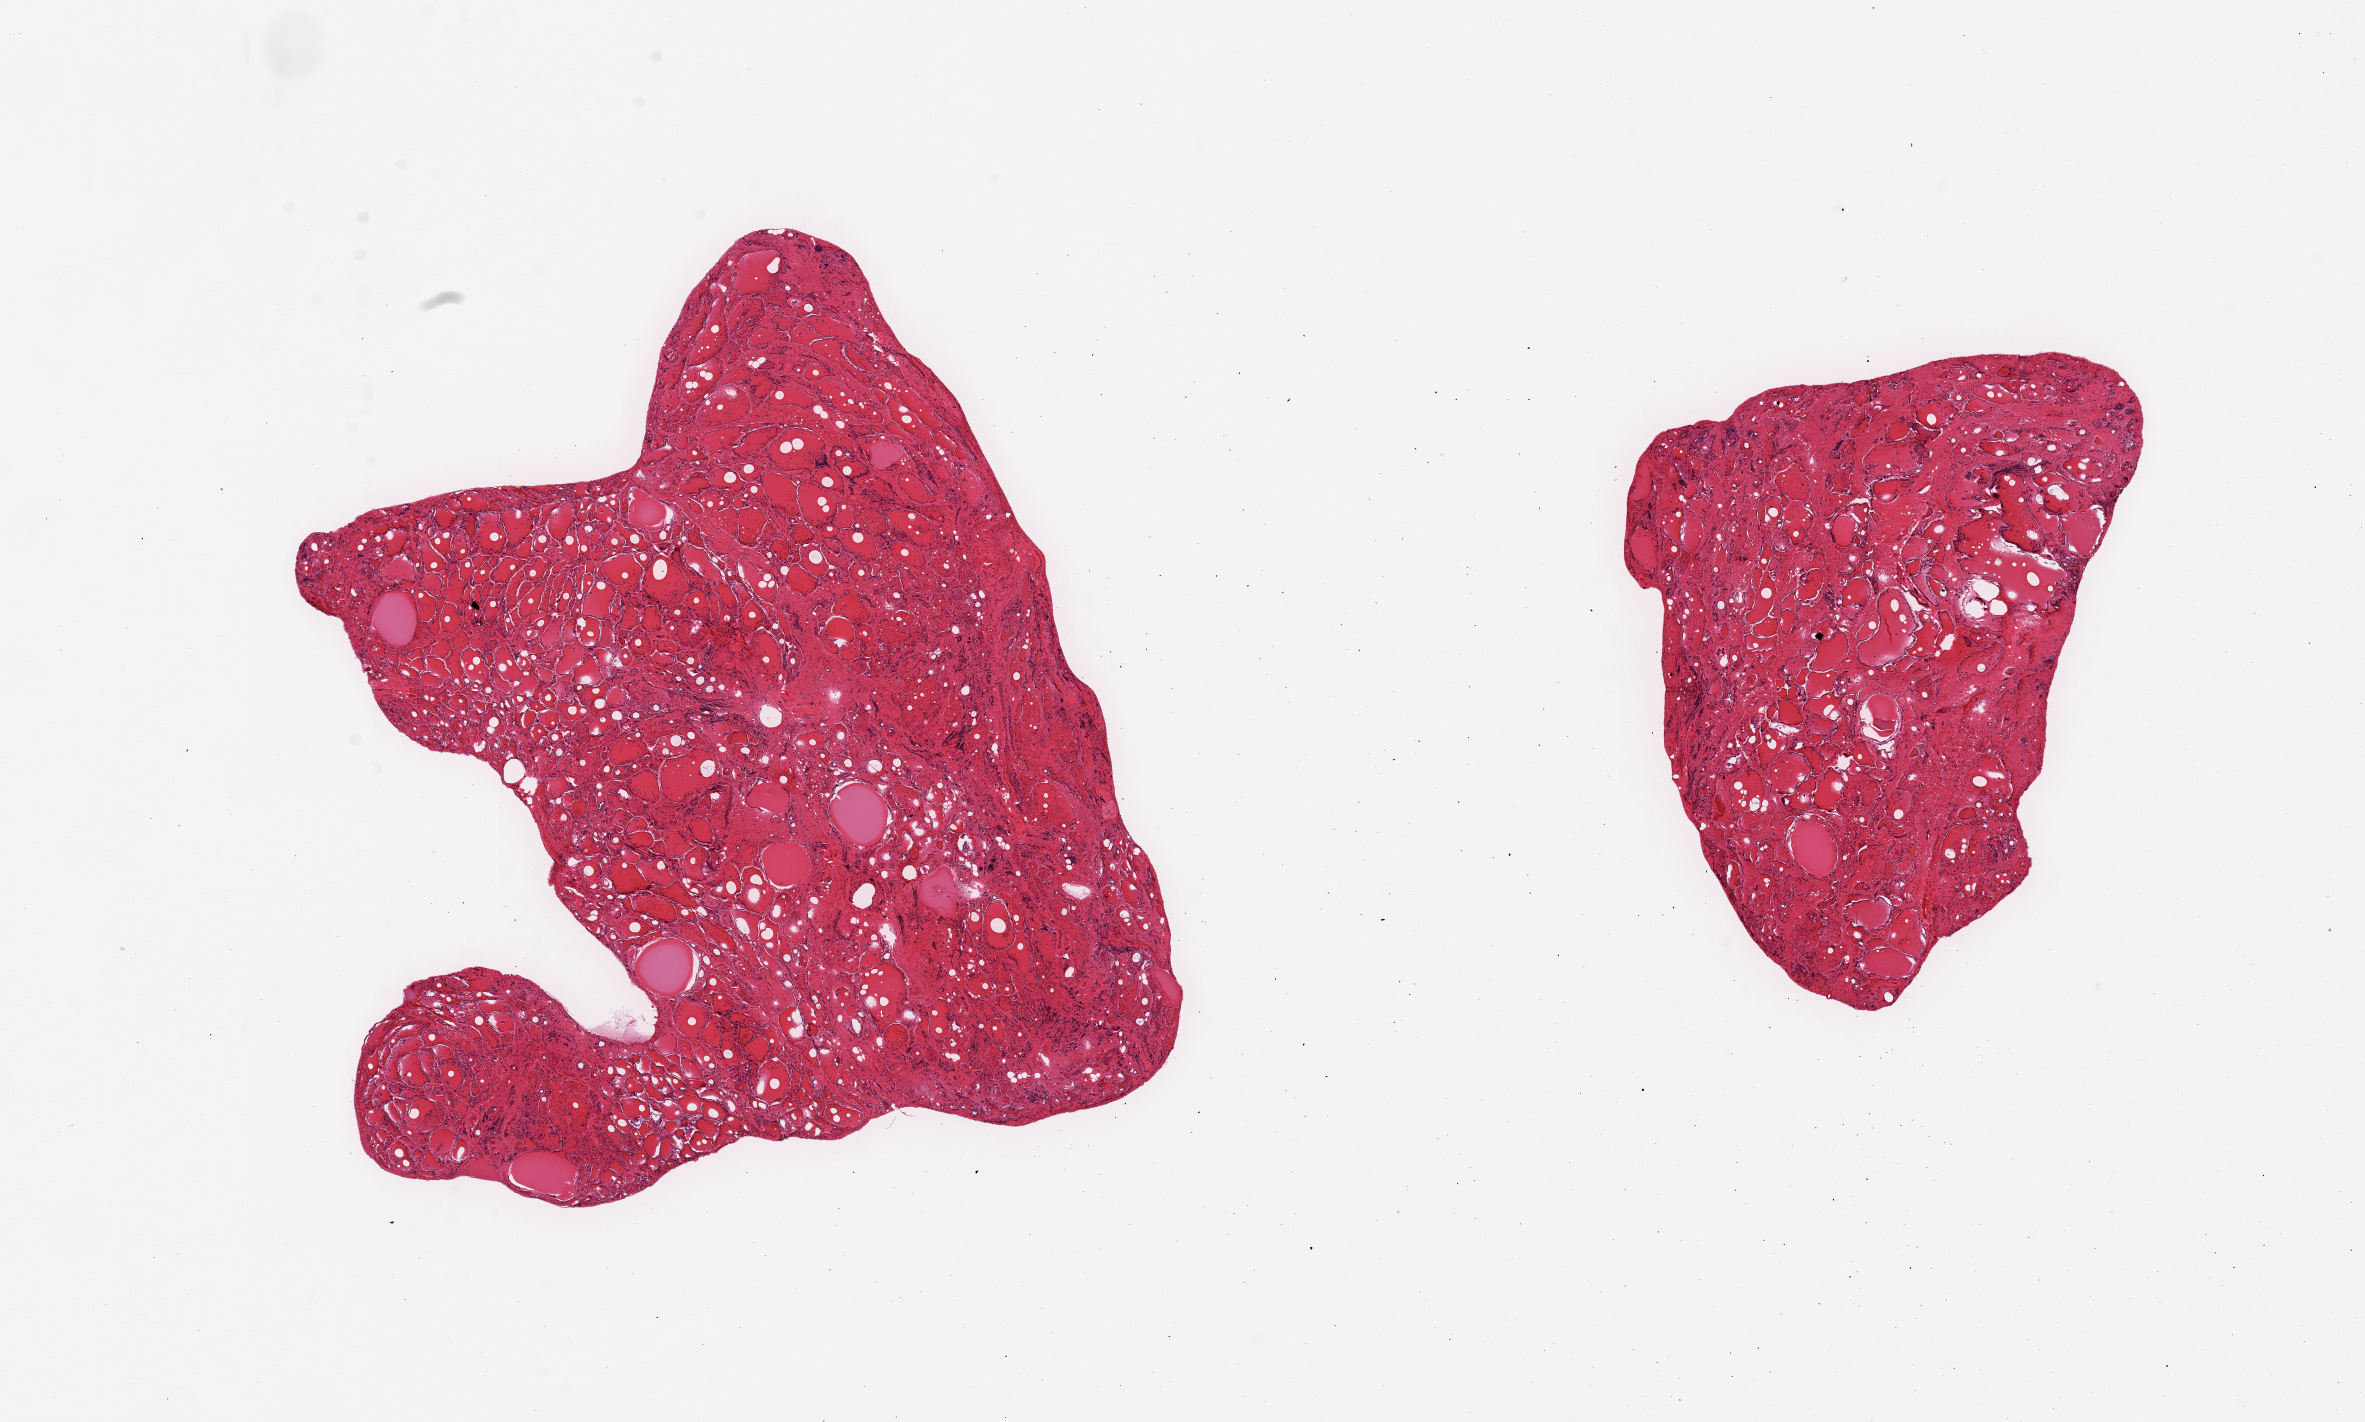
Haematoxylin and eosin whole-slide image — low-resolution overview of the scanned area, about 18.7 x 11.2 mm (acquisition: 20x scan); PAXgene-fixed paraffin-embedded (PFPE) section; section of thyroid (target tissue); donor tissue sample. Female donor.
Reviewer comment on this tissue sample: 2 pieces; no lesions; well trimmed.